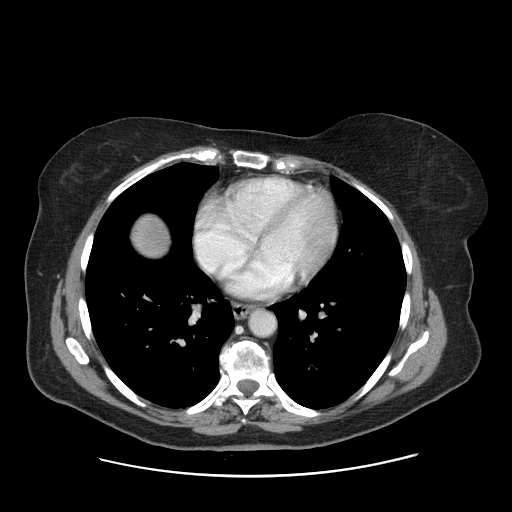
Contrast-enhanced abdominal CT, one axial slice. Position 156 of 161 along the scan axis. Intravenous contrast given. Soft-tissue window (W 400 / L 40 HU). 512 × 512 image matrix, field of view 398 × 398 mm. Female patient, age 62 years. Case-level facts recorded for this patient, not image findings: diagnosis: colorectal cancer liver metastases, imaged before liver resection; multiple liver metastases: no; largest metastasis: 2.5 cm; disease in both lobes: no.
Structures marked on this image (expert manual segmentation):
- liver: bounding box <133,217,168,255> (left, top, right, bottom; pixels)
- planned liver remnant (the part of the liver to remain after resection): <133,216,168,256>